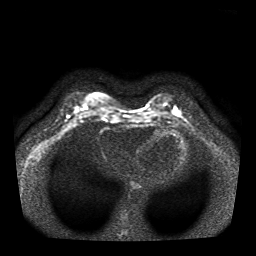
Breast MRI, one axial slice; slice 15 of 41 in the series (ordered by position); diffusion-weighted series; image 2 of 4 stored at this slice position (different b-values; order by instance number); 1.5 T; 5 mm slice thickness; 256 × 256 image matrix, field of view 330 × 330 mm. Female patient.
Annotated regions visible in this slice (outlined manually by an expert reader):
- tumour on diffusion-weighted imaging: bounding box <175,110,180,114> (left, top, right, bottom; pixels)